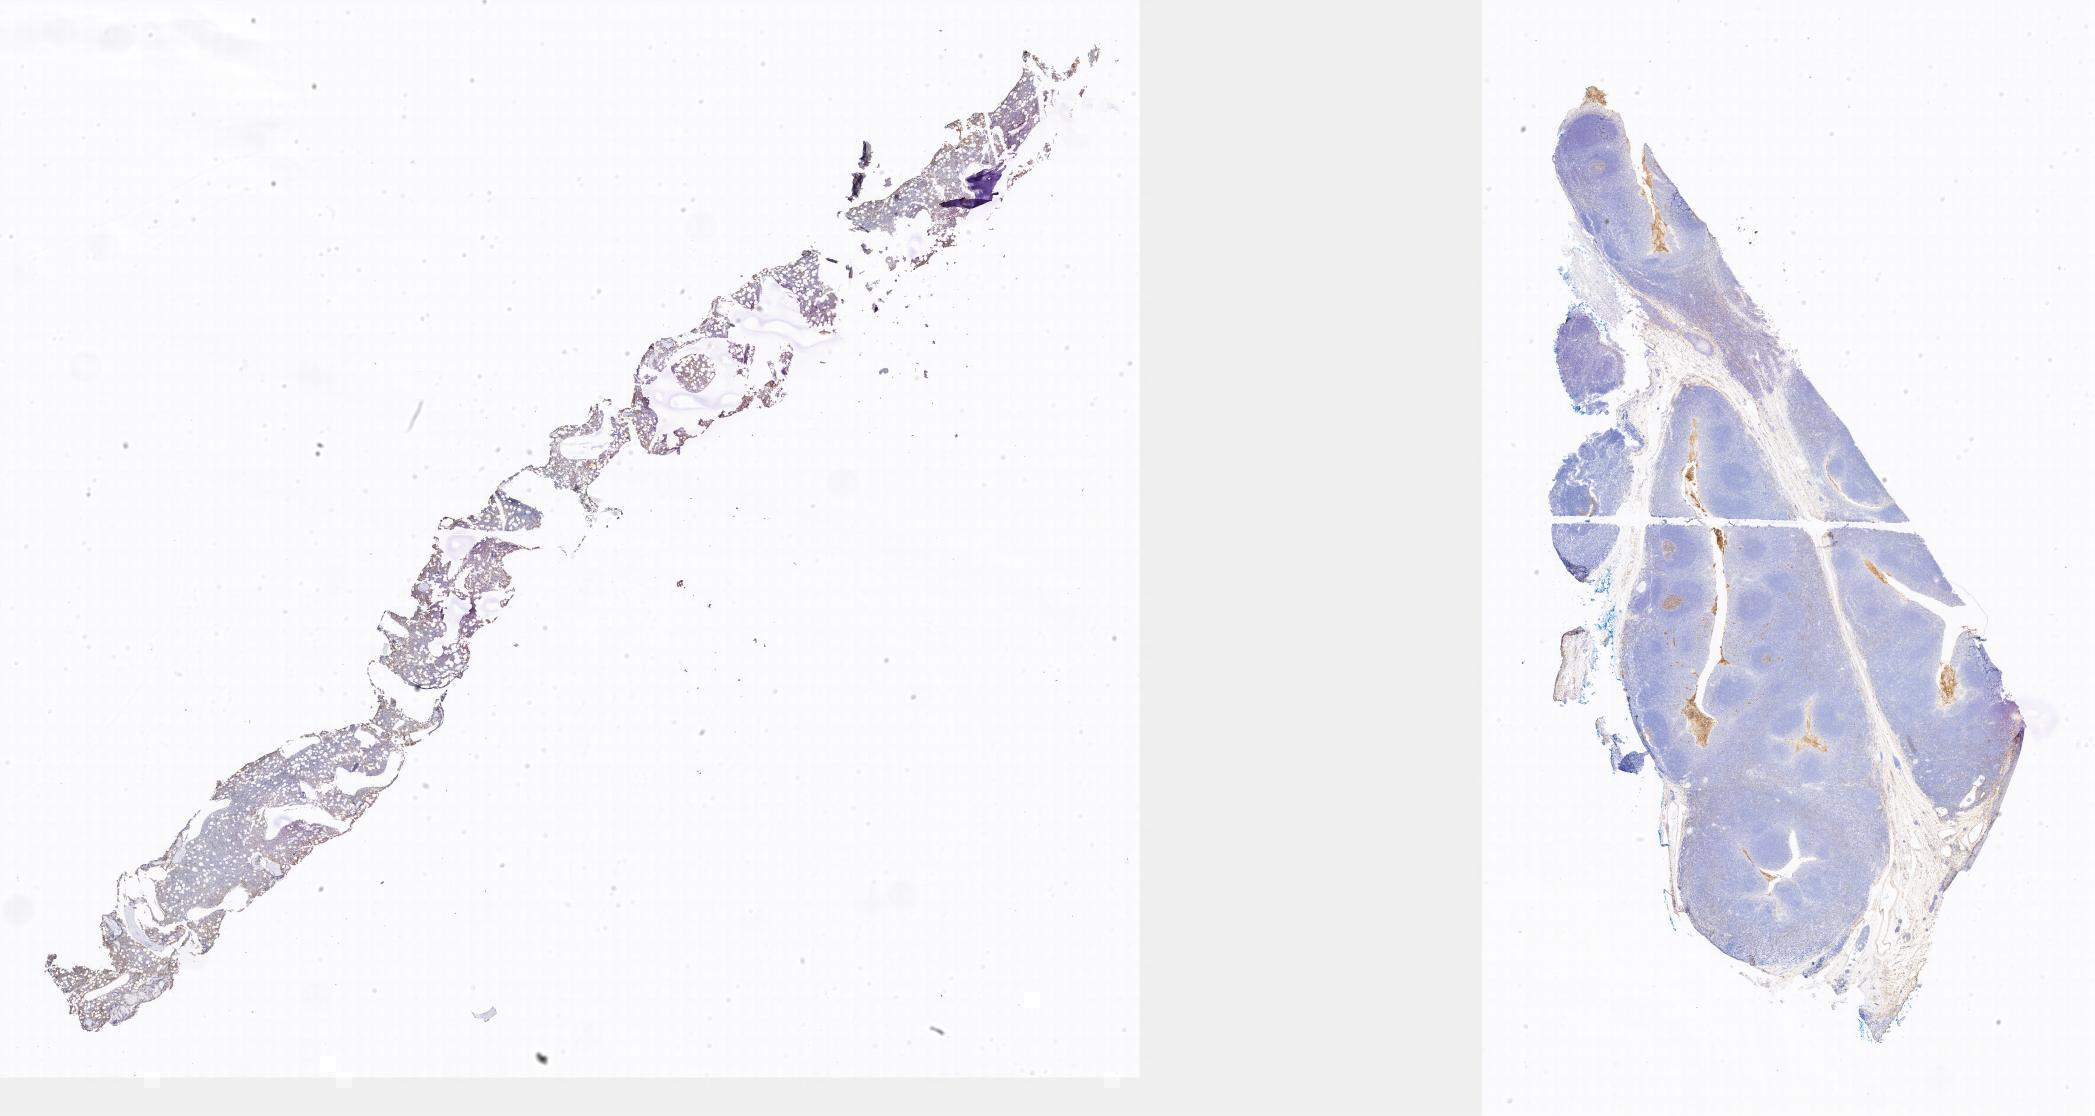
Whole-slide image, immunohistochemical stain for CD10 — low-resolution overview of the scanned area. Tumor tissue. Anatomic site: bone marrow. Male patient, age 20 years.
* histologic diagnosis: Diffuse large B-cell lymphoma, NOS